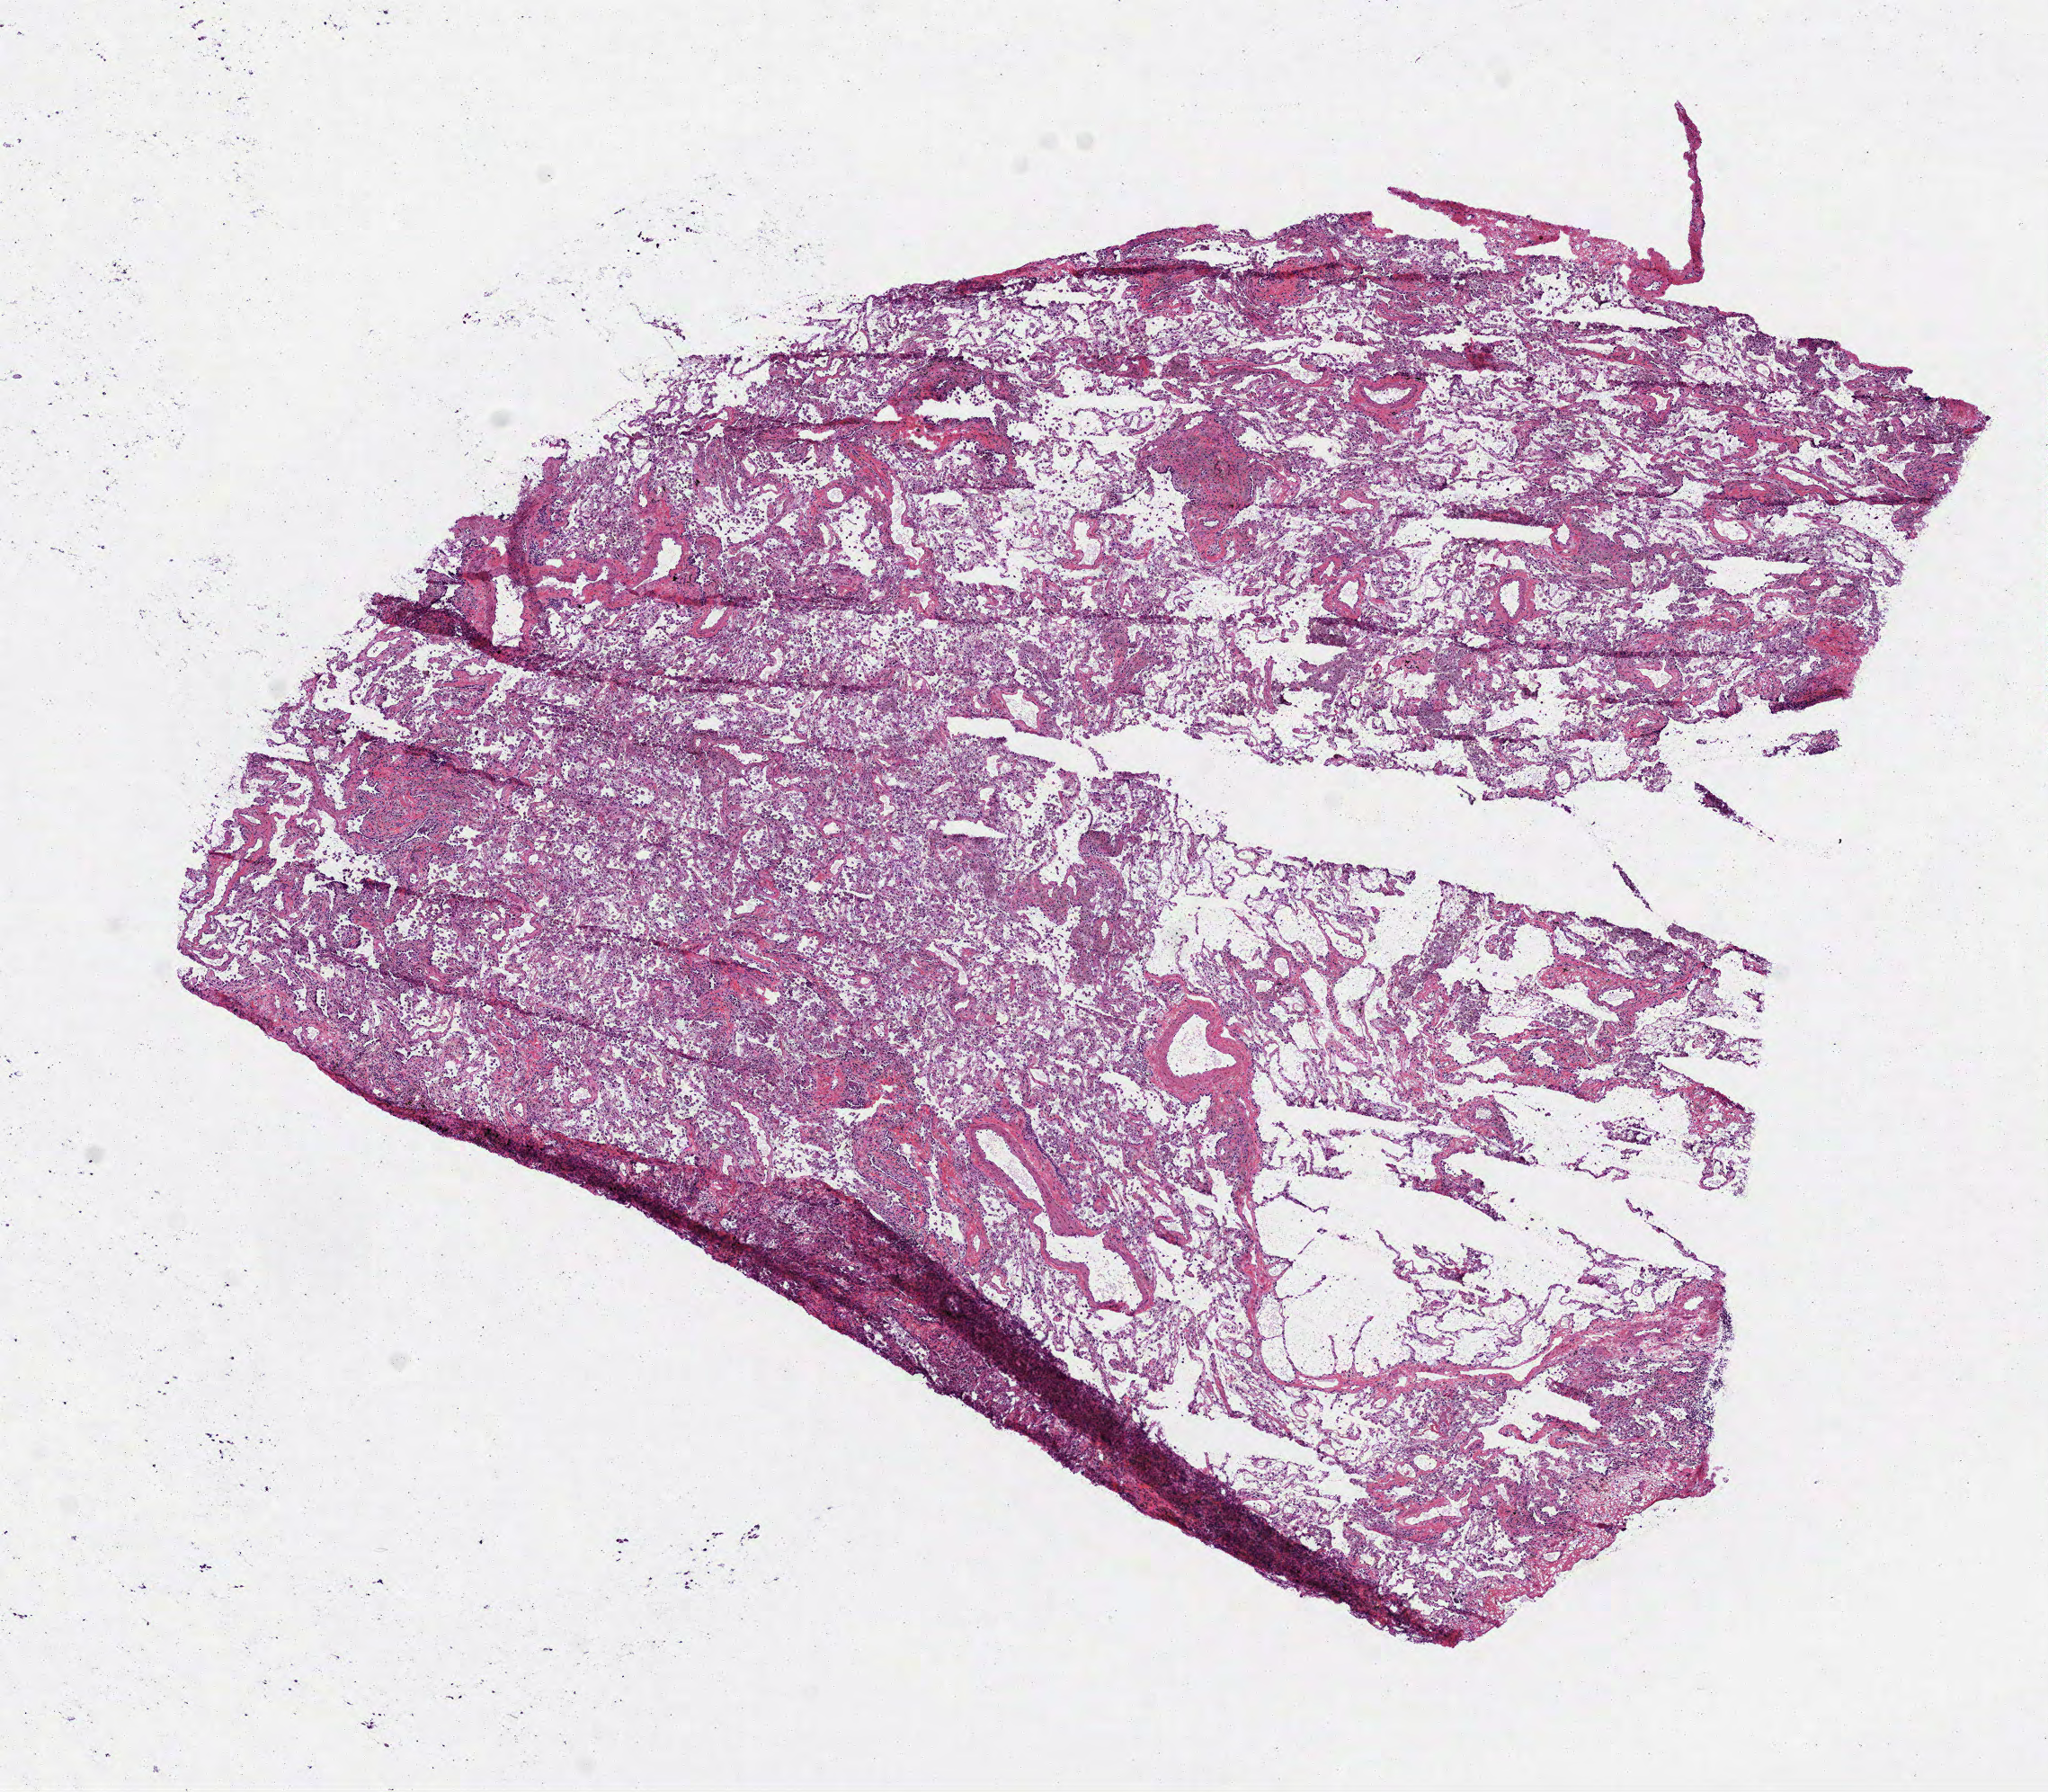
Digitized H&E tissue section (whole slide), low-resolution overview of the scanned area, about 9.2 x 8.0 mm (slide scanned at 40x); frozen section; solid tissue normal (non-tumour tissue) sample from the lung. Patient: male, age at initial diagnosis 58 years. Inflammatory infiltration, as recorded: lymphocyte infiltration 5%, monocyte infiltration 30%, neutrophil infiltration 0%.
- this section: solid tissue normal sample (biorepository sample class)
- patient diagnosis: Adenocarcinoma, NOS